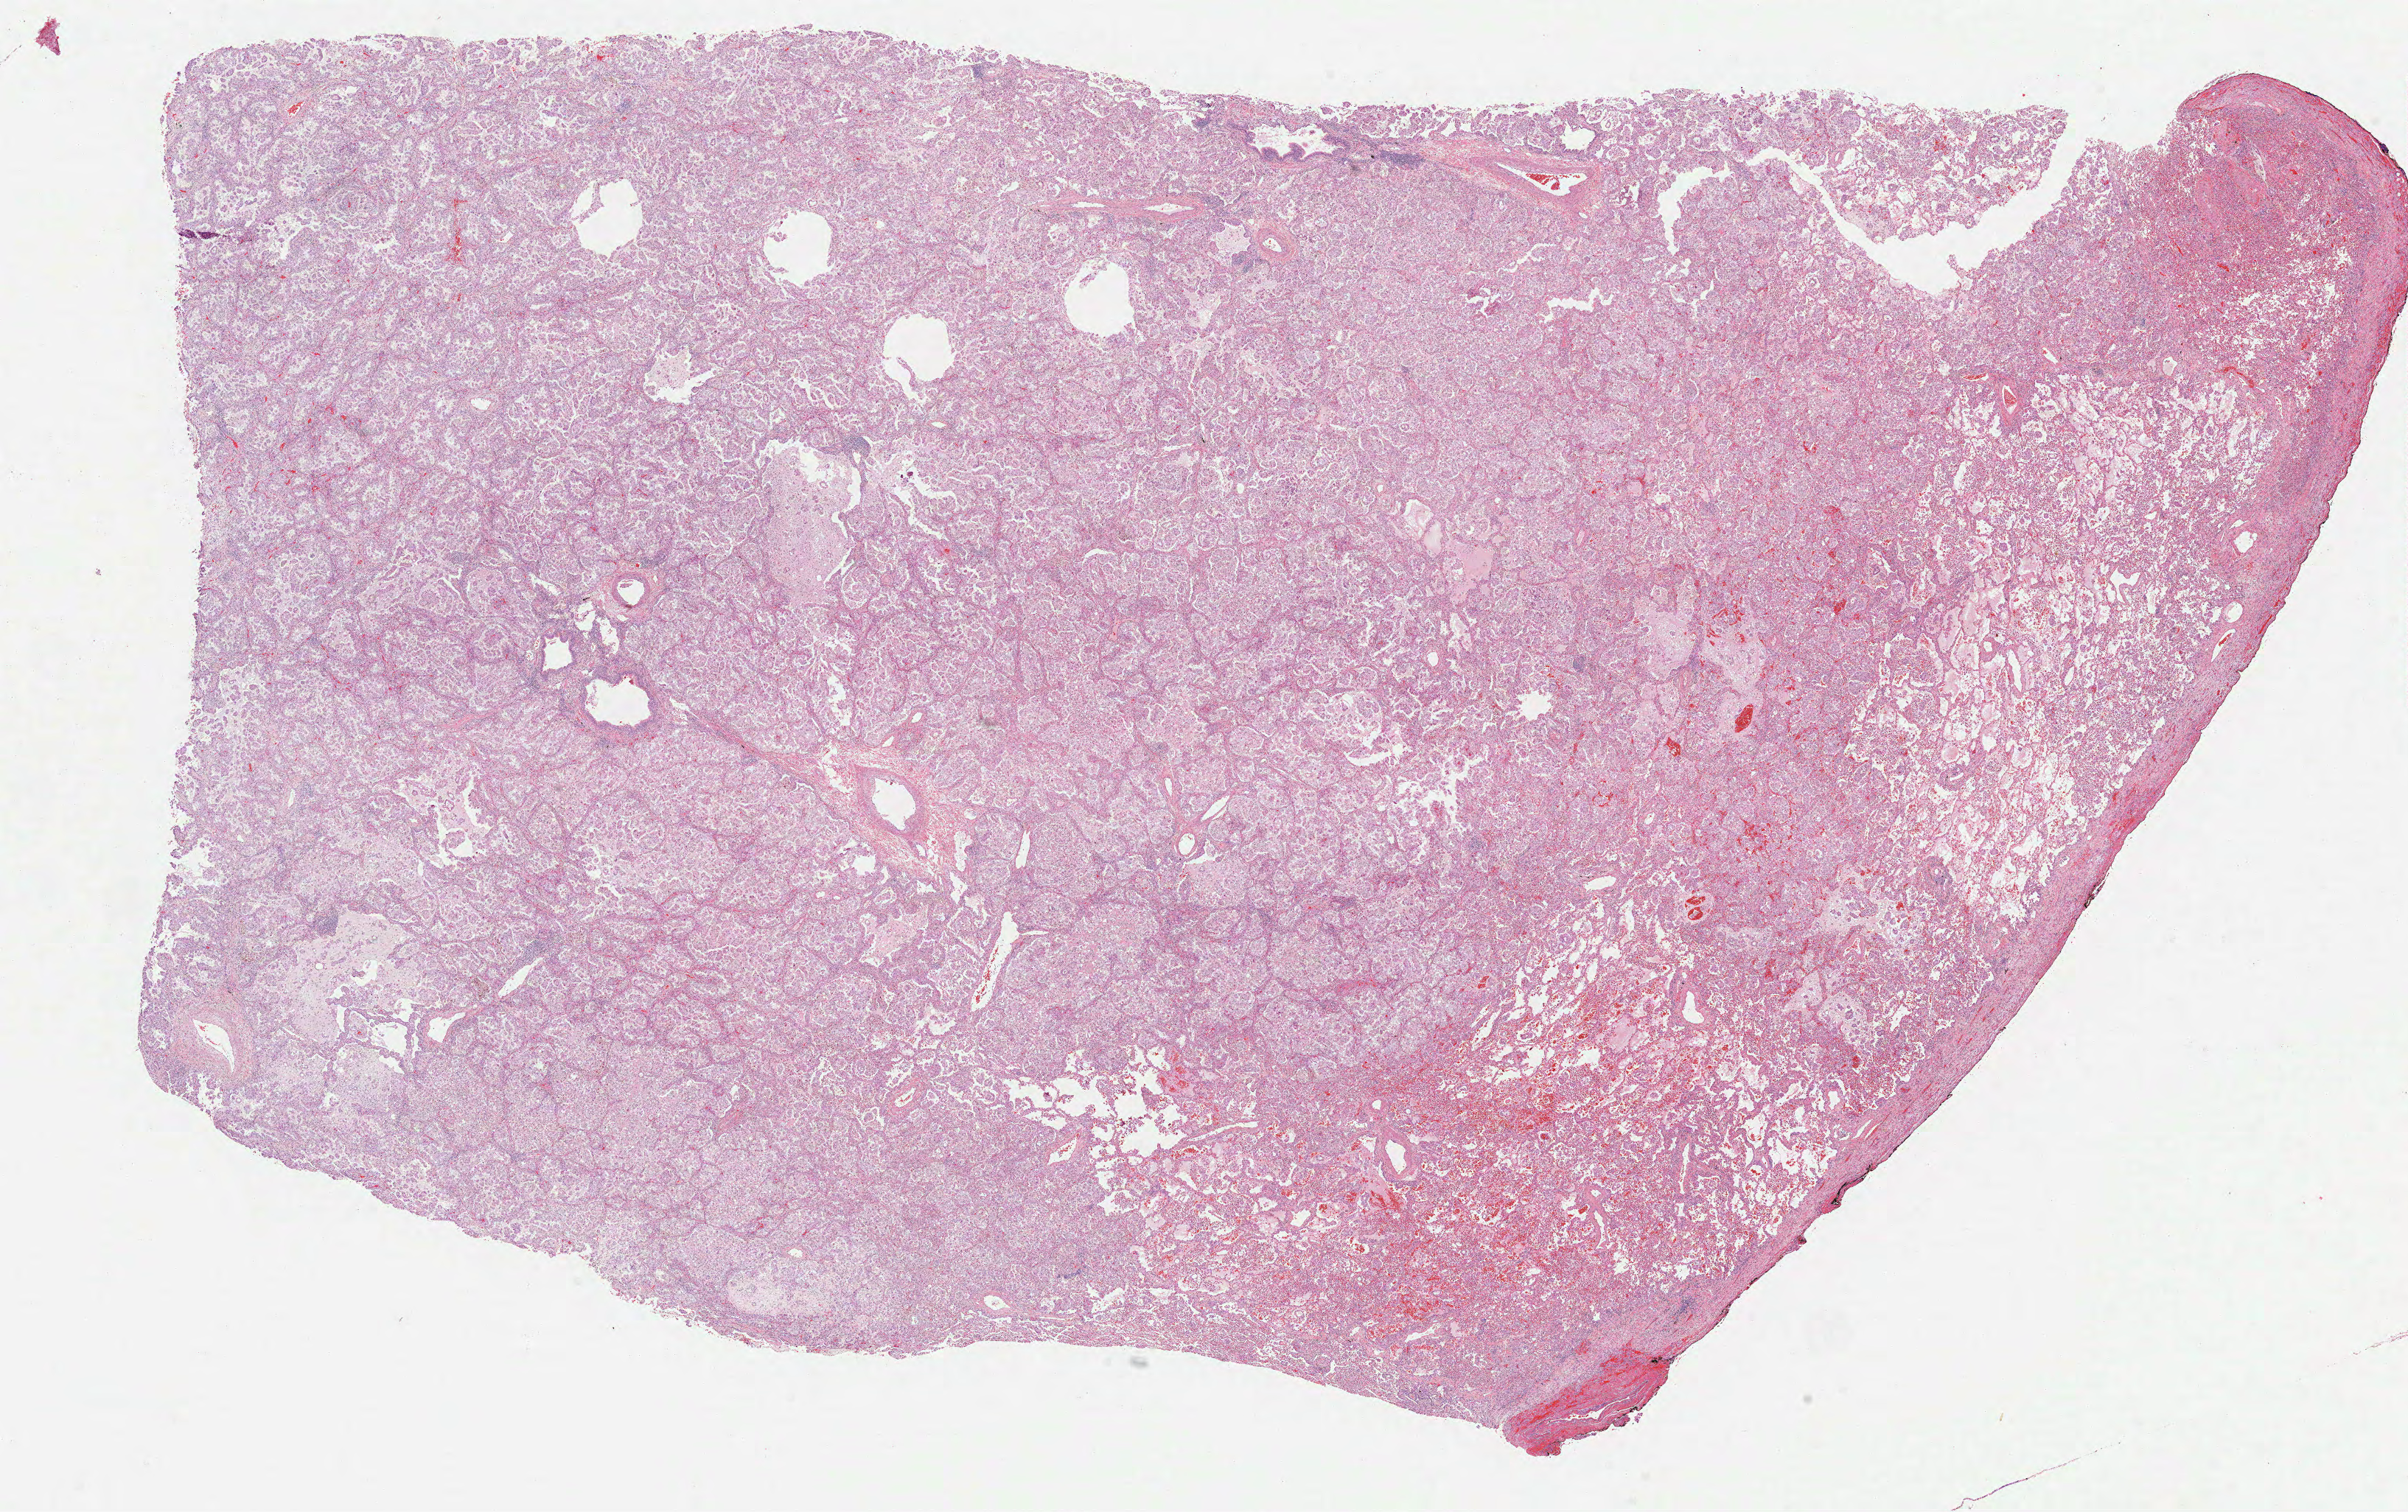
Whole-slide histology image, H&E, a low-resolution overview of the entire scanned area, about 26.3 x 16.5 mm (slide scanned at 40x), formalin-fixed paraffin-embedded (FFPE) diagnostic section, primary tumour sample from the lung. Patient: male, age at initial diagnosis 59 years.
Diagnosis: Adenocarcinoma, NOS (lower lobe, lung). Laterality: left. AJCC pathologic stage: IIIA.